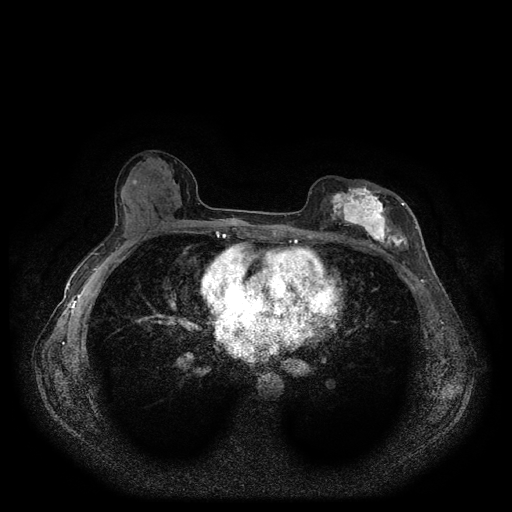
Breast MRI (dynamic contrast-enhanced, multi-phase), one axial slice; slice 54 of 116 in the series (ordered by position); dynamic contrast-enhanced series, time point 2 of 5 at this slice position (early post-contrast); 1.5 T; TE 2.6 ms, TR 5.3 ms; 2 mm slice thickness; 512 × 512 image matrix, field of view 350 × 350 mm. Female patient, age 51 years.
Outlined on this slice (semi-automatically segmented with operator editing):
- breast lesion (labelled 'tumour' in the annotation; benign lesions carry a separate 'benign' label): bounding box [x1, y1, x2, y2] px = [324, 185, 412, 251]